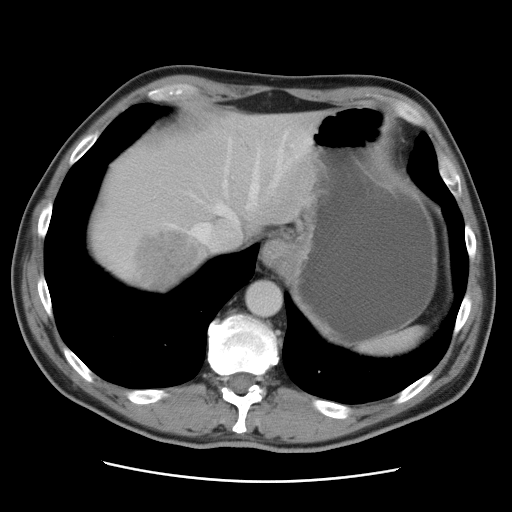
Contrast-enhanced abdominal CT, one axial slice; slice 76 of 89 in the series (ordered by position); 120 kVp; intravenous contrast given; soft-tissue window (W 400 / L 40 HU); 512 × 512 image matrix, field of view 366 × 366 mm. Male patient, age 59 years. From the clinical record (not read from this slice): diagnosis: colorectal cancer liver metastases, imaged before liver resection; multiple liver metastases: yes; largest metastasis: 0.6 cm; disease in both lobes: yes.
Annotated regions visible in this slice (expert manual segmentation):
- hepatic veins: bounding box <189,132,288,255> (left, top, right, bottom; pixels)
- liver: <89,112,328,293>
- planned liver remnant (the part of the liver to remain after resection): <130,112,328,241>
- liver metastasis: <137,233,204,291>